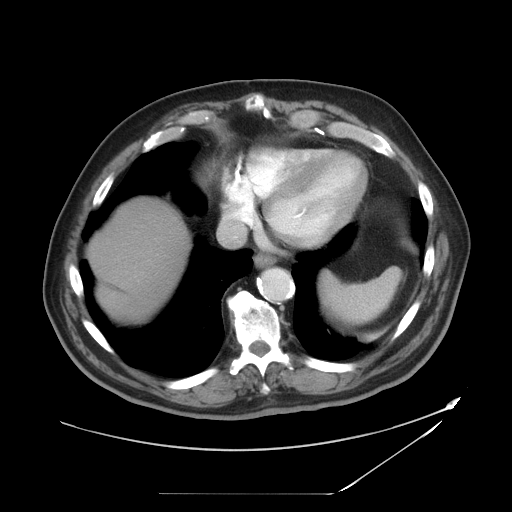
Contrast-enhanced abdominal CT, one axial slice. Slice 41 of 49 in the series (ordered by position). Reconstruction kernel STANDARD. 120 kVp. Intravenous contrast given. Soft-tissue window (W 400 / L 40 HU). 5 mm slice thickness. 512 × 512 image matrix, field of view 461 × 461 mm. Male patient, age 72 years. From the clinical record (not read from this slice): diagnosis: colorectal cancer liver metastases, imaged before liver resection; multiple liver metastases: no; largest metastasis: 2.5 cm; disease in both lobes: no.
Annotated regions visible in this slice (expert manual segmentation):
- liver: bounding box (x1, y1, x2, y2) in pixels: (90, 200, 187, 321)
- planned liver remnant (the part of the liver to remain after resection): (91, 200, 187, 321)